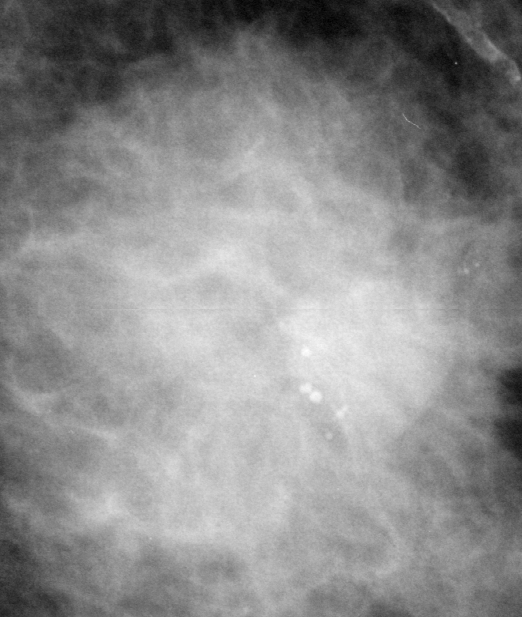
Crop from a digitized film mammogram around one marked abnormality, left breast, MLO view, BI-RADS breast density category 1 (scale 1–4).
- Mass, shape lobulated, margins microlobulated; BI-RADS assessment category 5; subtlety rating 5 on a 1 (subtle) to 5 (obvious) scale; pathology (as recorded): malignant.